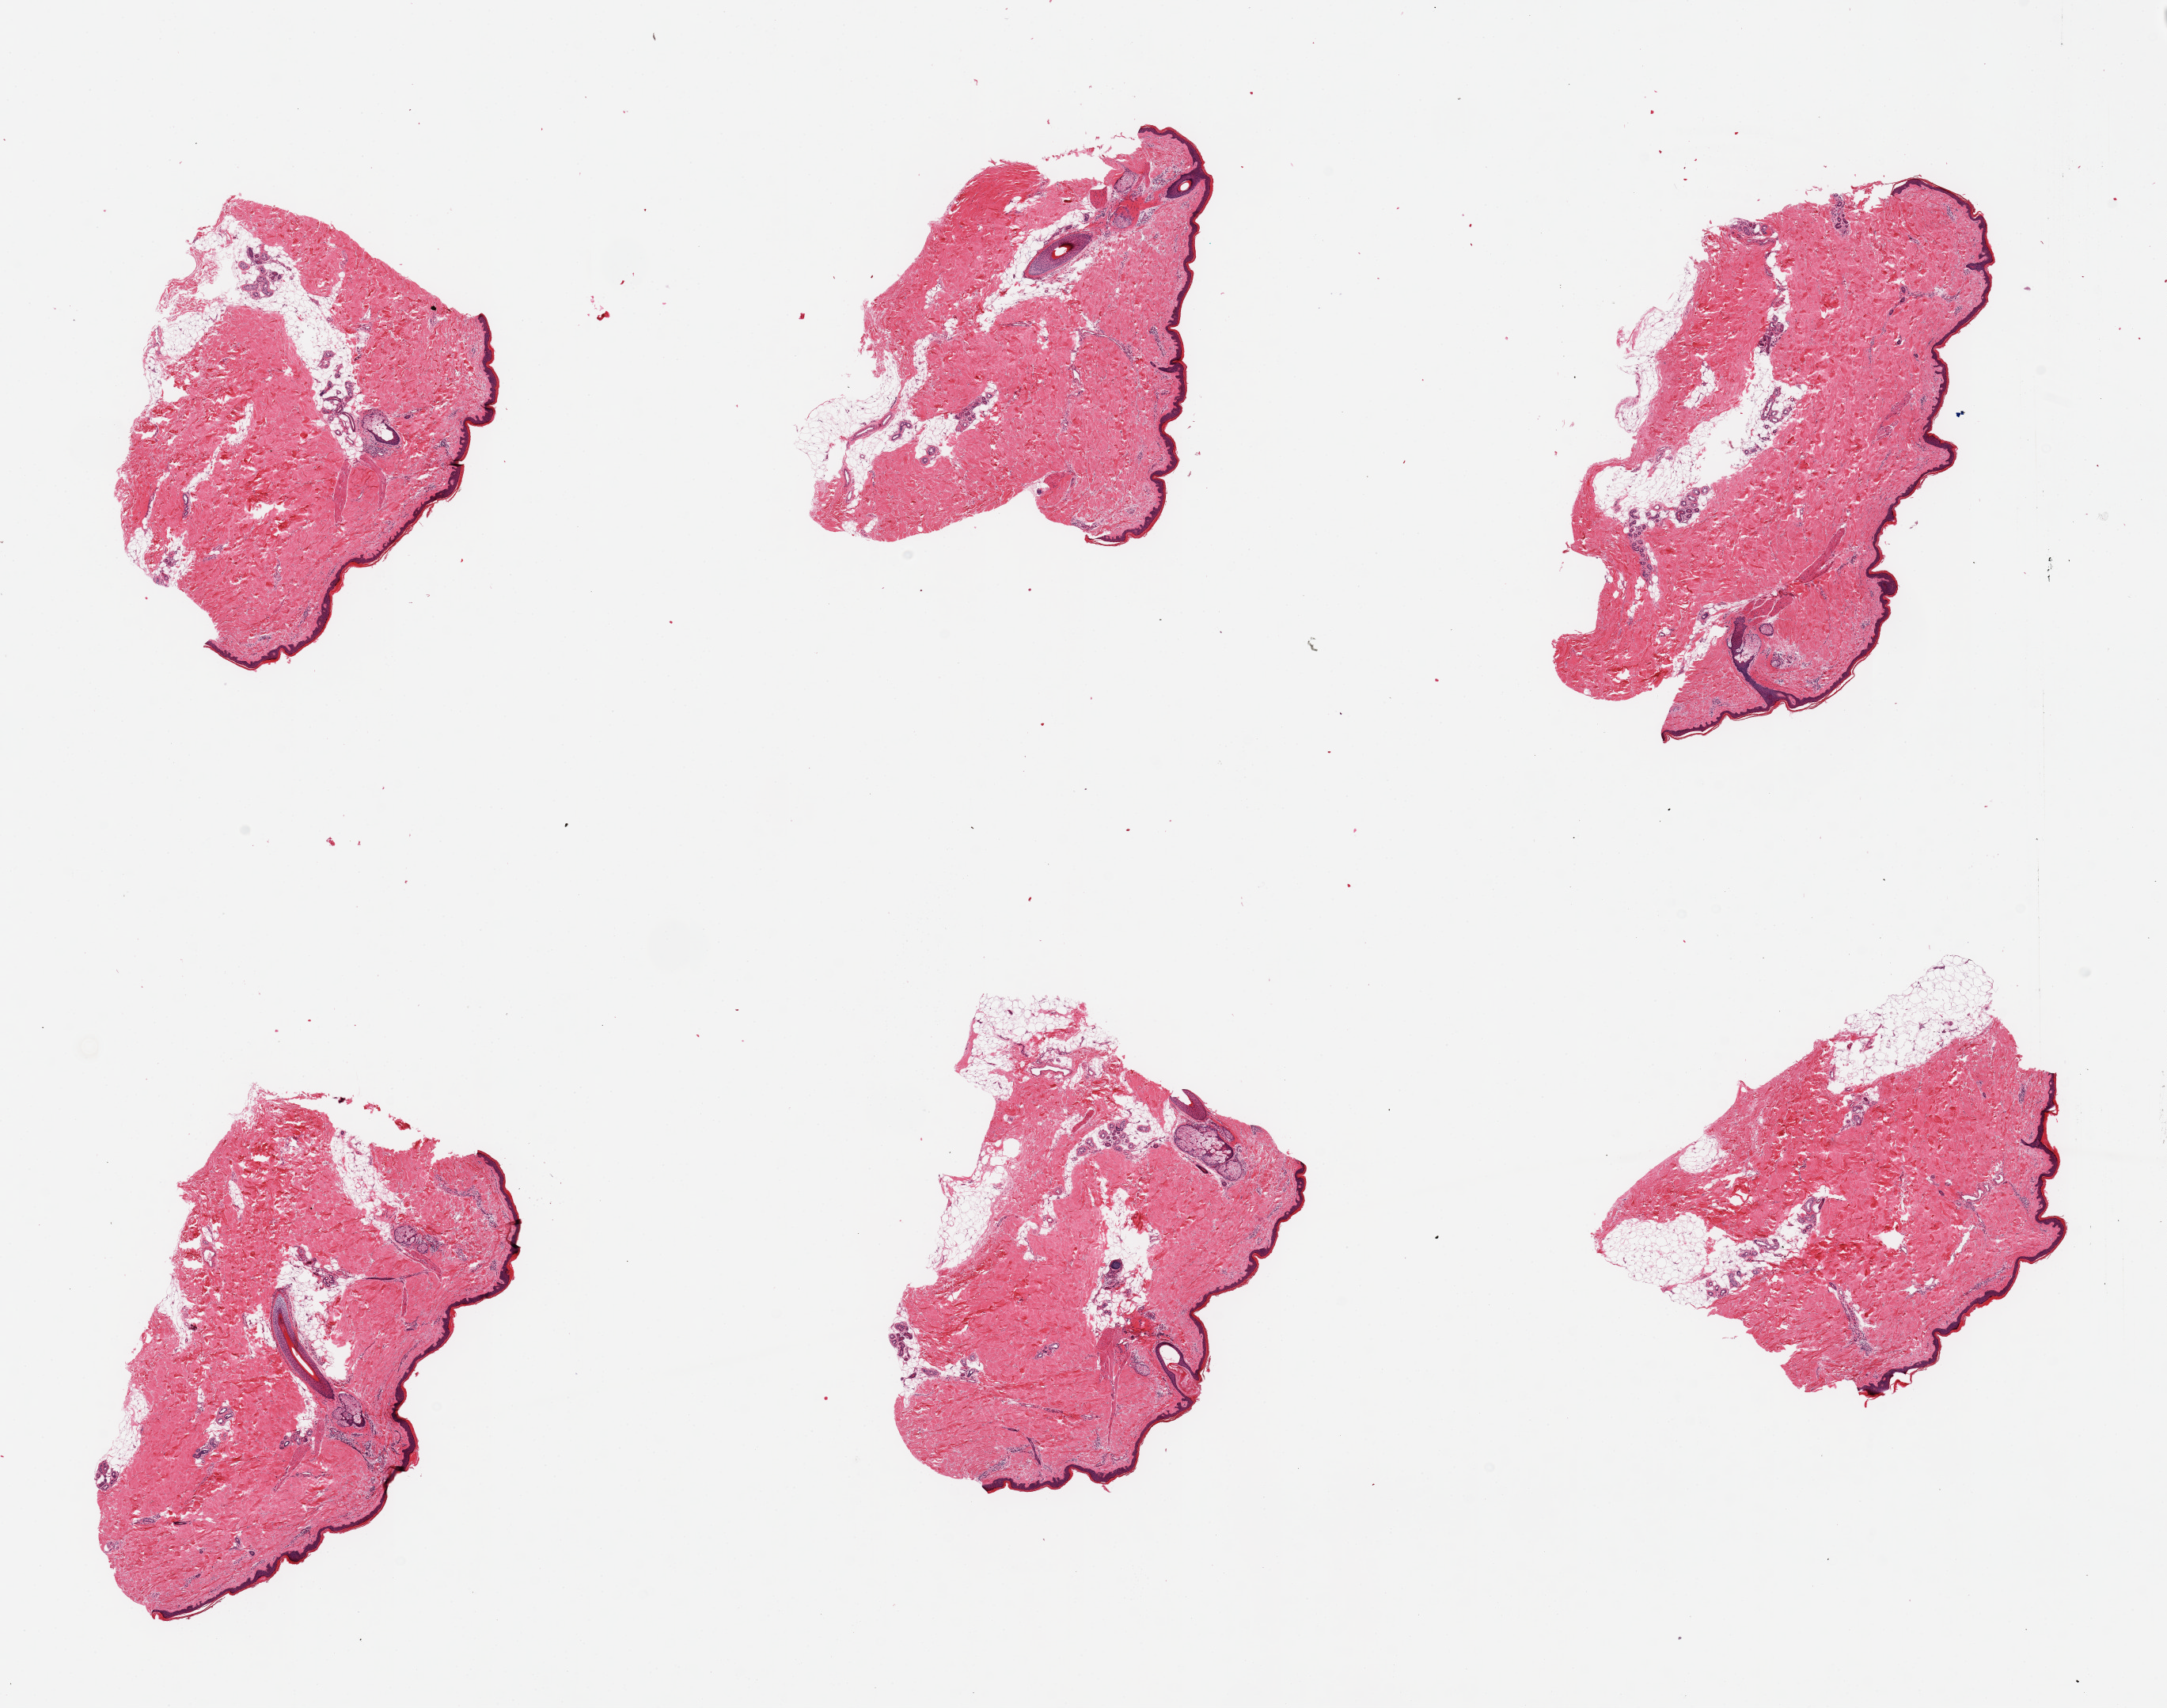
Whole-slide image, H&E stain, brightfield, a low-resolution overview of the entire scanned area, about 21.7 x 17.1 mm (from a 20x scan), PAXgene-fixed, paraffin-embedded tissue, sampled site (target tissue): skin of lower leg, donor tissue sample. Donor sex: male.
Pathologist's review note for this sample: 6 pieces; well trimmed; 10% dermal fat; epidermis 33um thick.